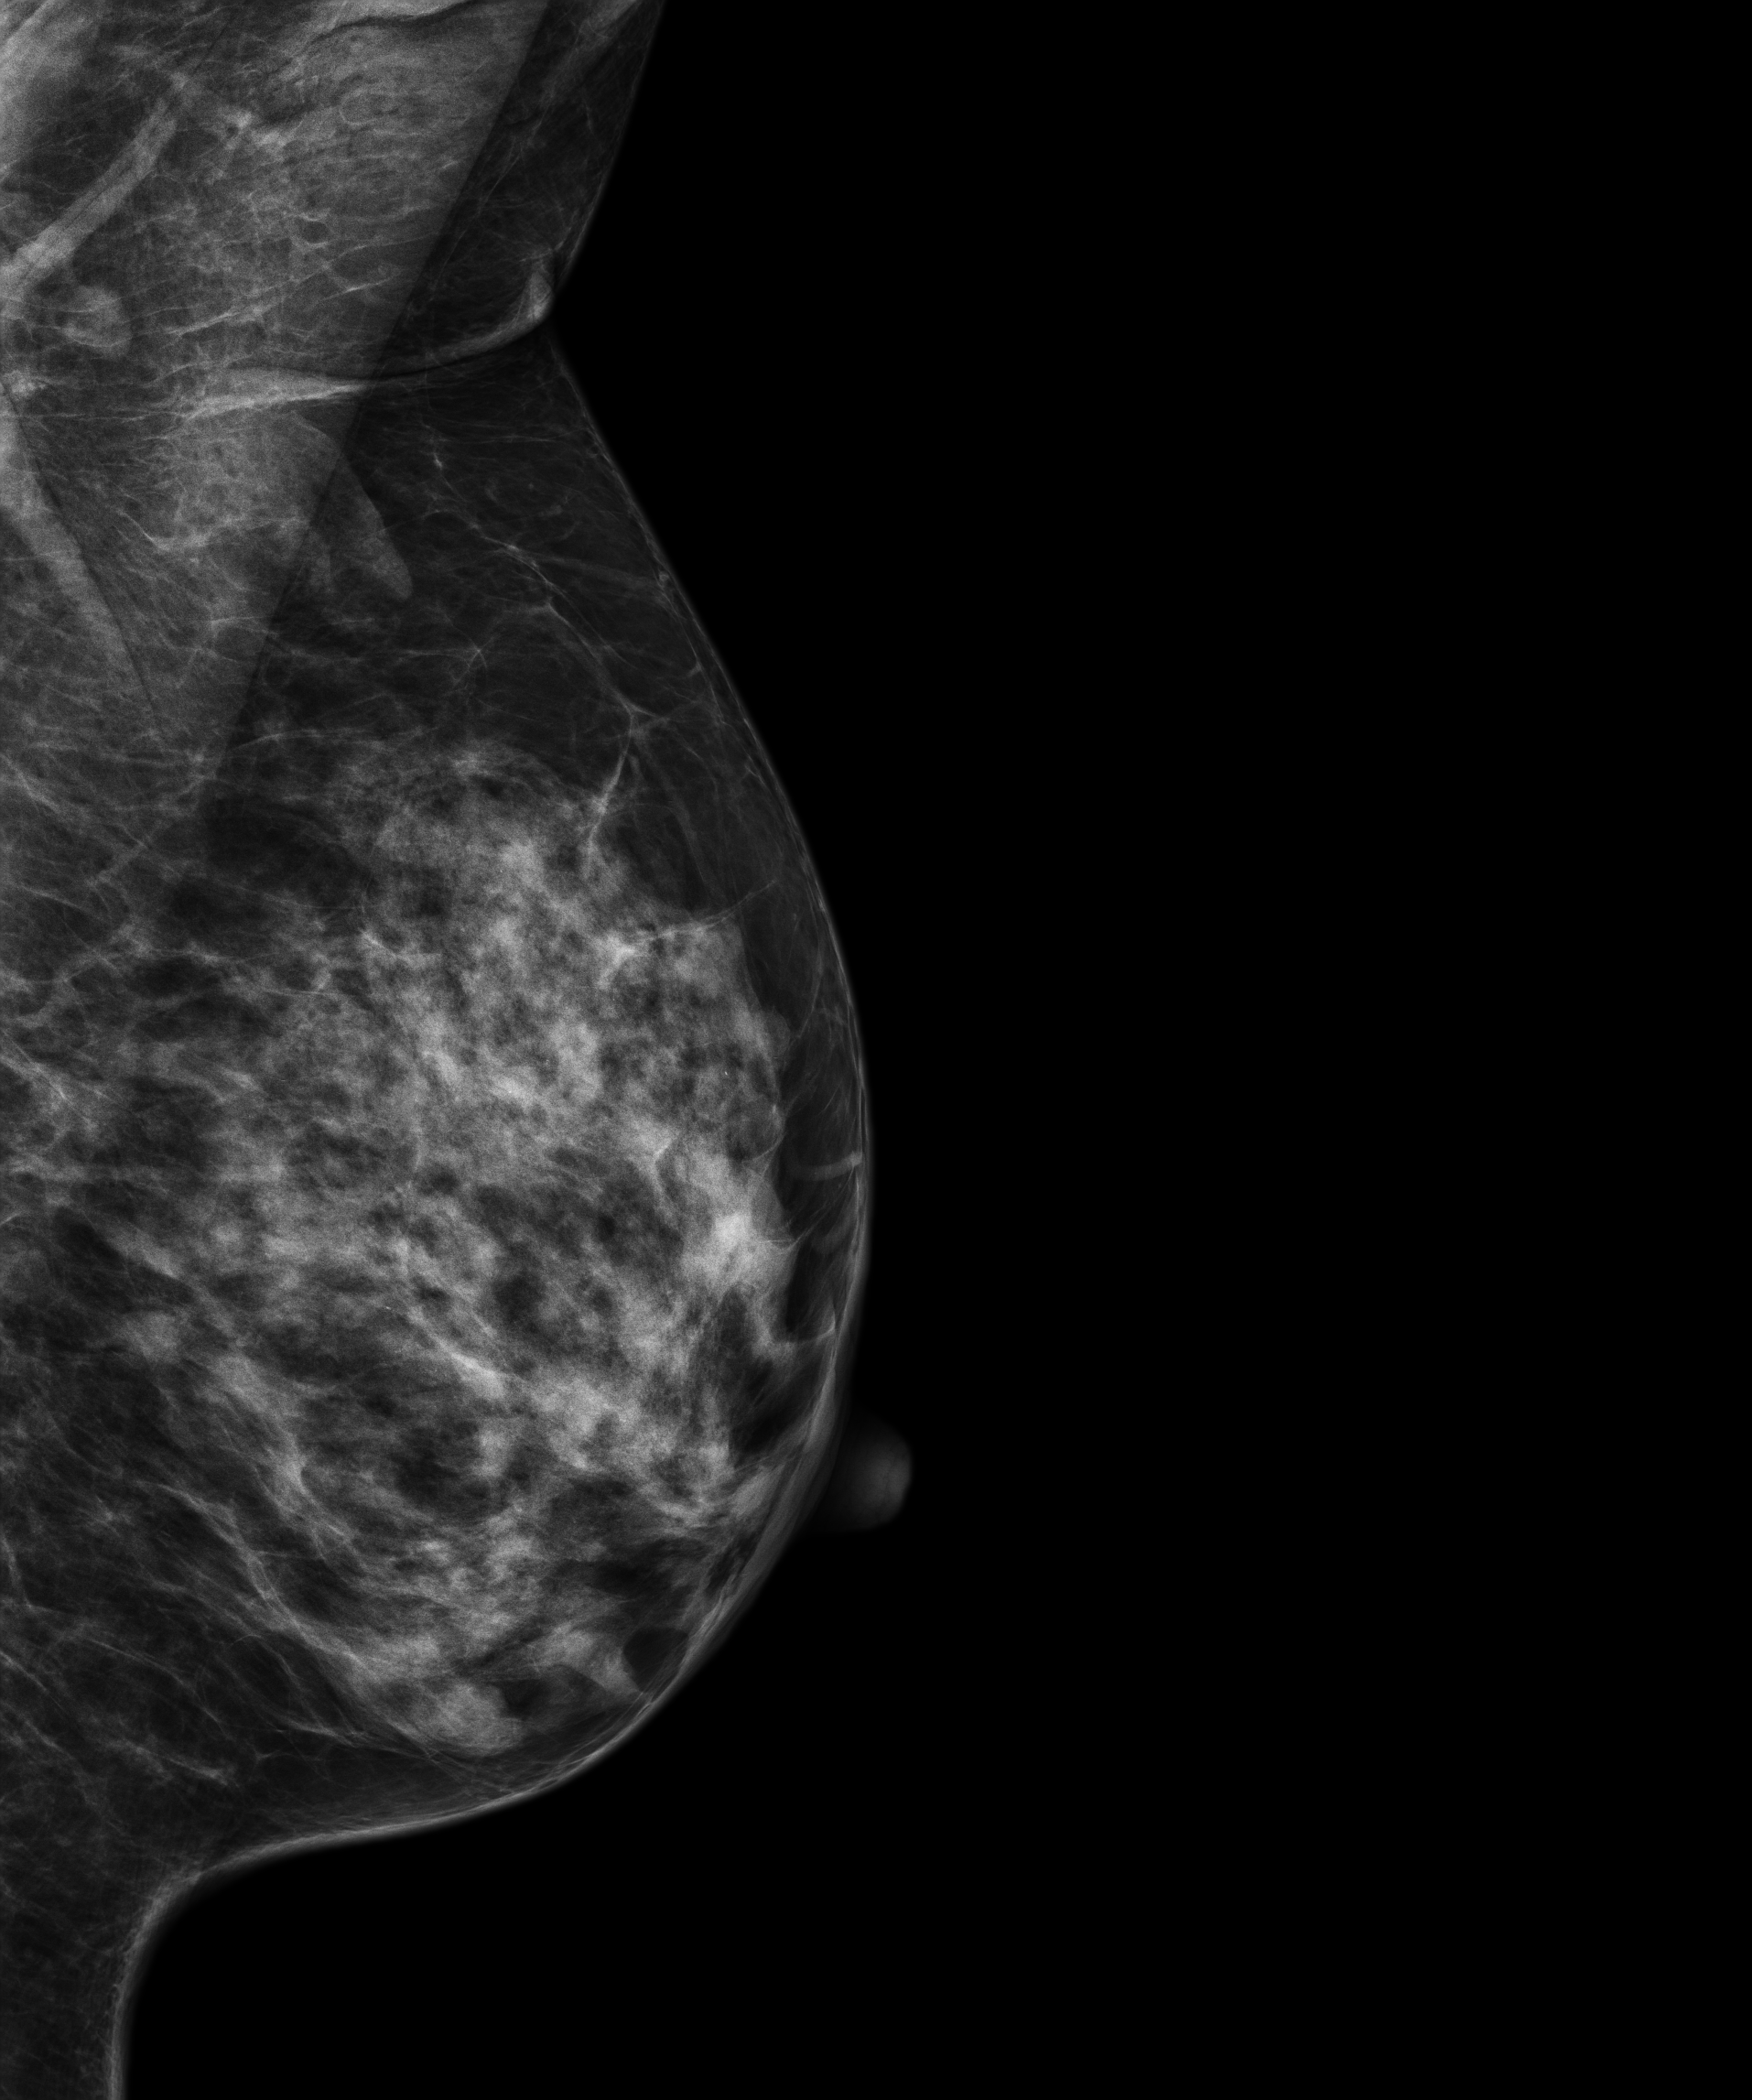
Digital mammogram (FFDM); left breast; medio-lateral oblique projection; annual screening mammography examination. Female patient, age 58 years.
- breast density at the screening exam (both breasts): heterogeneously dense (BI-RADS density category c)
- final BI-RADS assessment for this screening round (tomosynthesis exam, both breasts): category 1
- recall: no recall after this screen